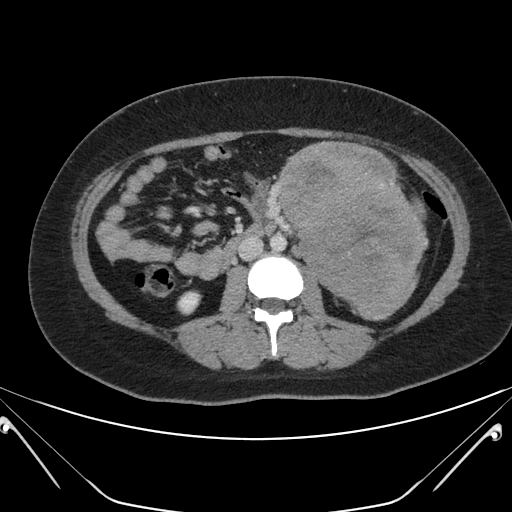
Contrast-enhanced abdominal CT, one axial slice; position 98 of 168 along the scan axis; intravenous contrast given; soft-tissue window (W 400 / L 40 HU); 512 × 512 image matrix, field of view 394 × 394 mm. Female patient, age 26 years. From the clinical record (not read from this slice): diagnosis: adrenocortical carcinoma; tumour side: left adrenal; tumour size at pathology: 28 cm; Ki-67 index: 20 %; stage (as recorded): 2.
Outlined on this slice (semi-automatic segmentation, software-assisted and operator-edited):
- mass: bounding box (x1, y1, x2, y2) in pixels: (281, 143, 424, 315)